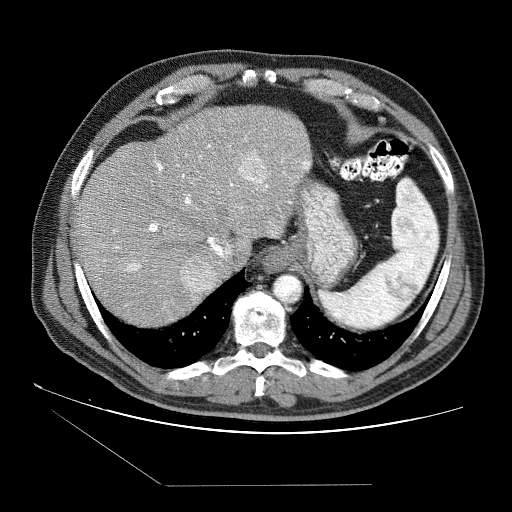
Contrast-enhanced abdominal CT (liver protocol), one axial slice; position 65 of 87 along the scan axis; reconstruction kernel STANDARD; 120 kVp; soft-tissue window (W 400 / L 40 HU); 512 × 512 image matrix, field of view 400 × 400 mm. From the clinical record (not read from this slice): diagnosis: hepatocellular carcinoma (patient treated with transarterial chemoembolisation; whether this scan precedes or follows treatment is not stated here); TNM stage (as recorded): Stage-II; Child-Pugh class: B; tumour differentiation: no biopsy; tumour nodularity: multinodular.
Annotated regions visible in this slice (semi-automatically segmented with operator editing):
- liver parenchyma outside the tumour (the mass and vessels are separate outlines, so this box may not span the whole liver): bounding box <76,106,312,326> (left, top, right, bottom; pixels)
- mass: <178,153,268,292>
- liver vessels: <84,137,310,306>